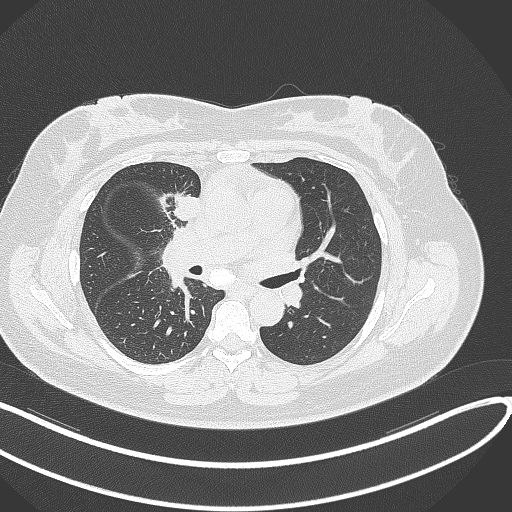
Chest CT, one axial slice; reconstruction kernel B70f; 120 kVp; lung window (W 1500 / L -600 HU); 512 × 512 image matrix. Patient: female, 46 years. Case-level facts recorded for this patient, not image findings: clinical TNM (as recorded): T2a N1 M0.
Structures marked on this image (bounding box drawn by a radiologist):
- lung tumour (recorded histology: adenocarcinoma): bounding box (x1, y1, x2, y2) in pixels: (168, 189, 201, 225)